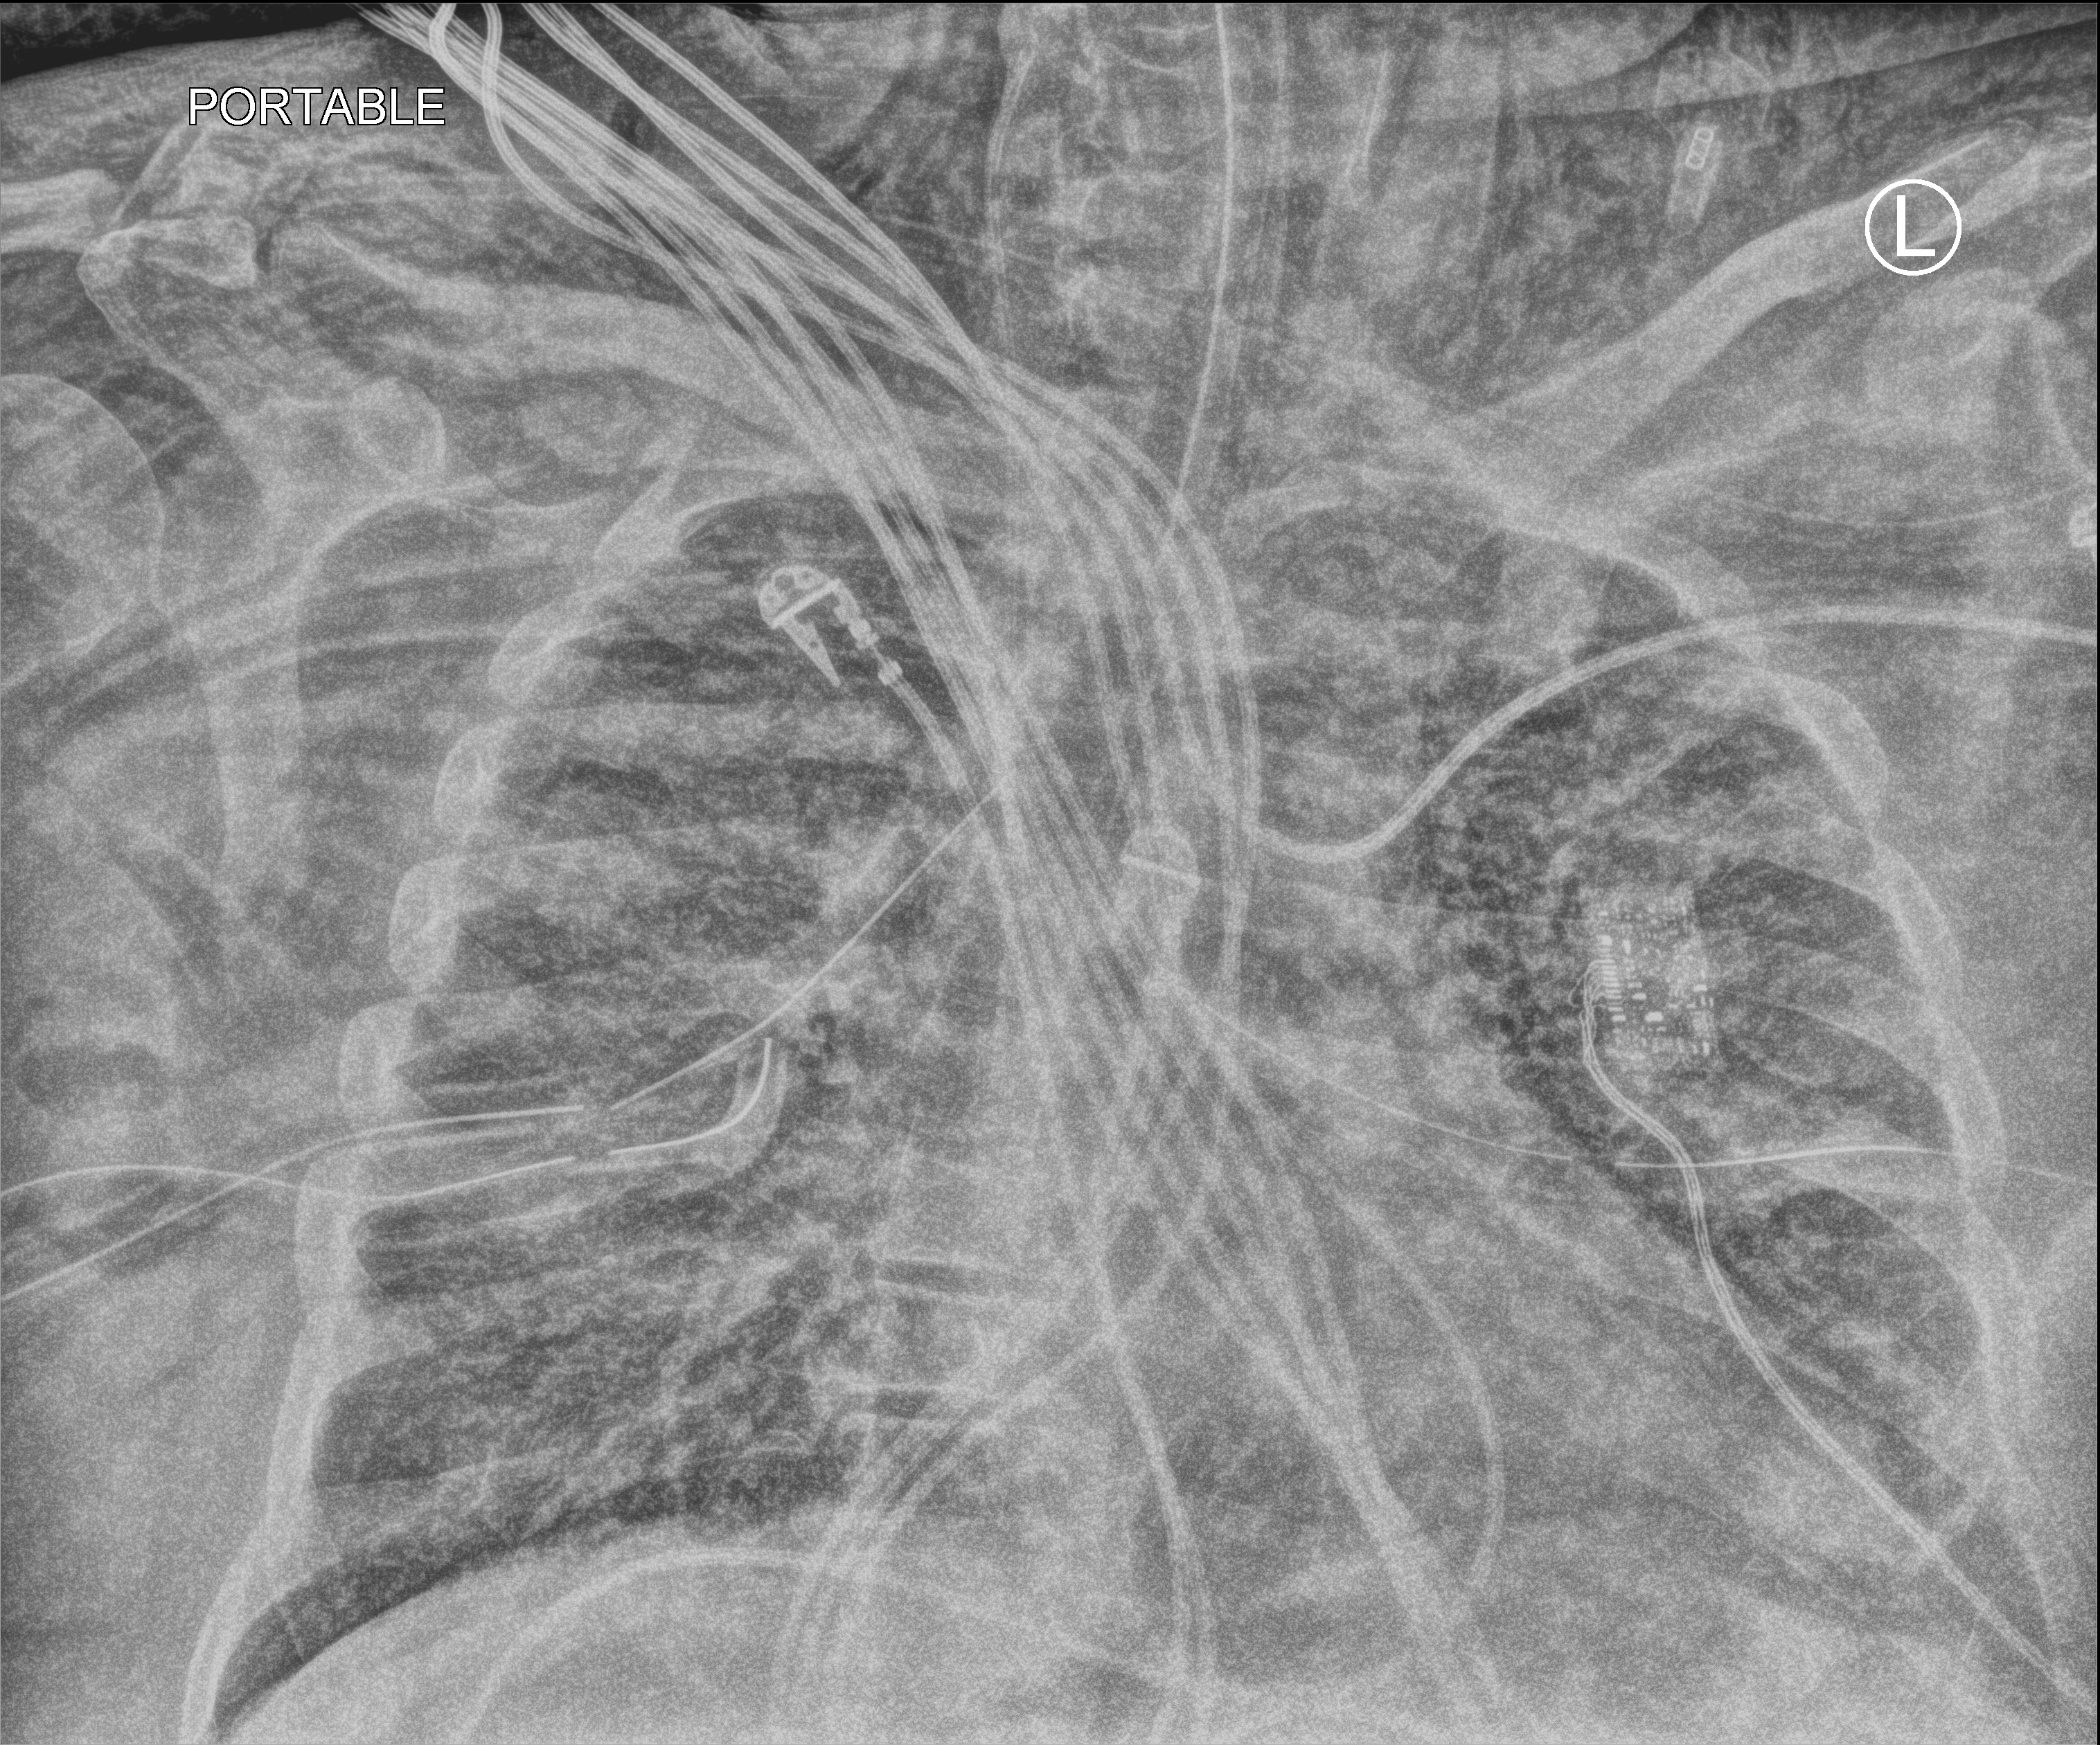
Portable chest radiograph, anteroposterior (AP) projection. Adult patient hospitalised with COVID-19, age 18–59 years.
Admission-level facts for this patient (not findings on this image; timing relative to this image not recorded):
- admitted to intensive care during this hospital stay: yes